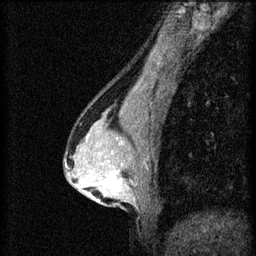
Breast MRI (dynamic contrast-enhanced), one sagittal slice; position 34 of 60 along the scan axis; 3 images stored at this slice position (order not interpretable as contrast timing); 1.5 T; TE 4.2 ms, TR 8.2 ms; 2 mm slice thickness; 256 × 256 image matrix, field of view 180 × 180 mm. Female patient, age 44 years.
Structures marked on this image (semi-automatically segmented with operator editing):
- analysis volume of interest (the breast-tissue region the enhancement analysis was run in; not a lesion): bounding box (x1, y1, x2, y2) in pixels: (94, 162, 141, 205)
- tumour enhancement mask (voxels above the 70 % enhancement threshold inside the analysis volume of interest): (108, 172, 119, 191)